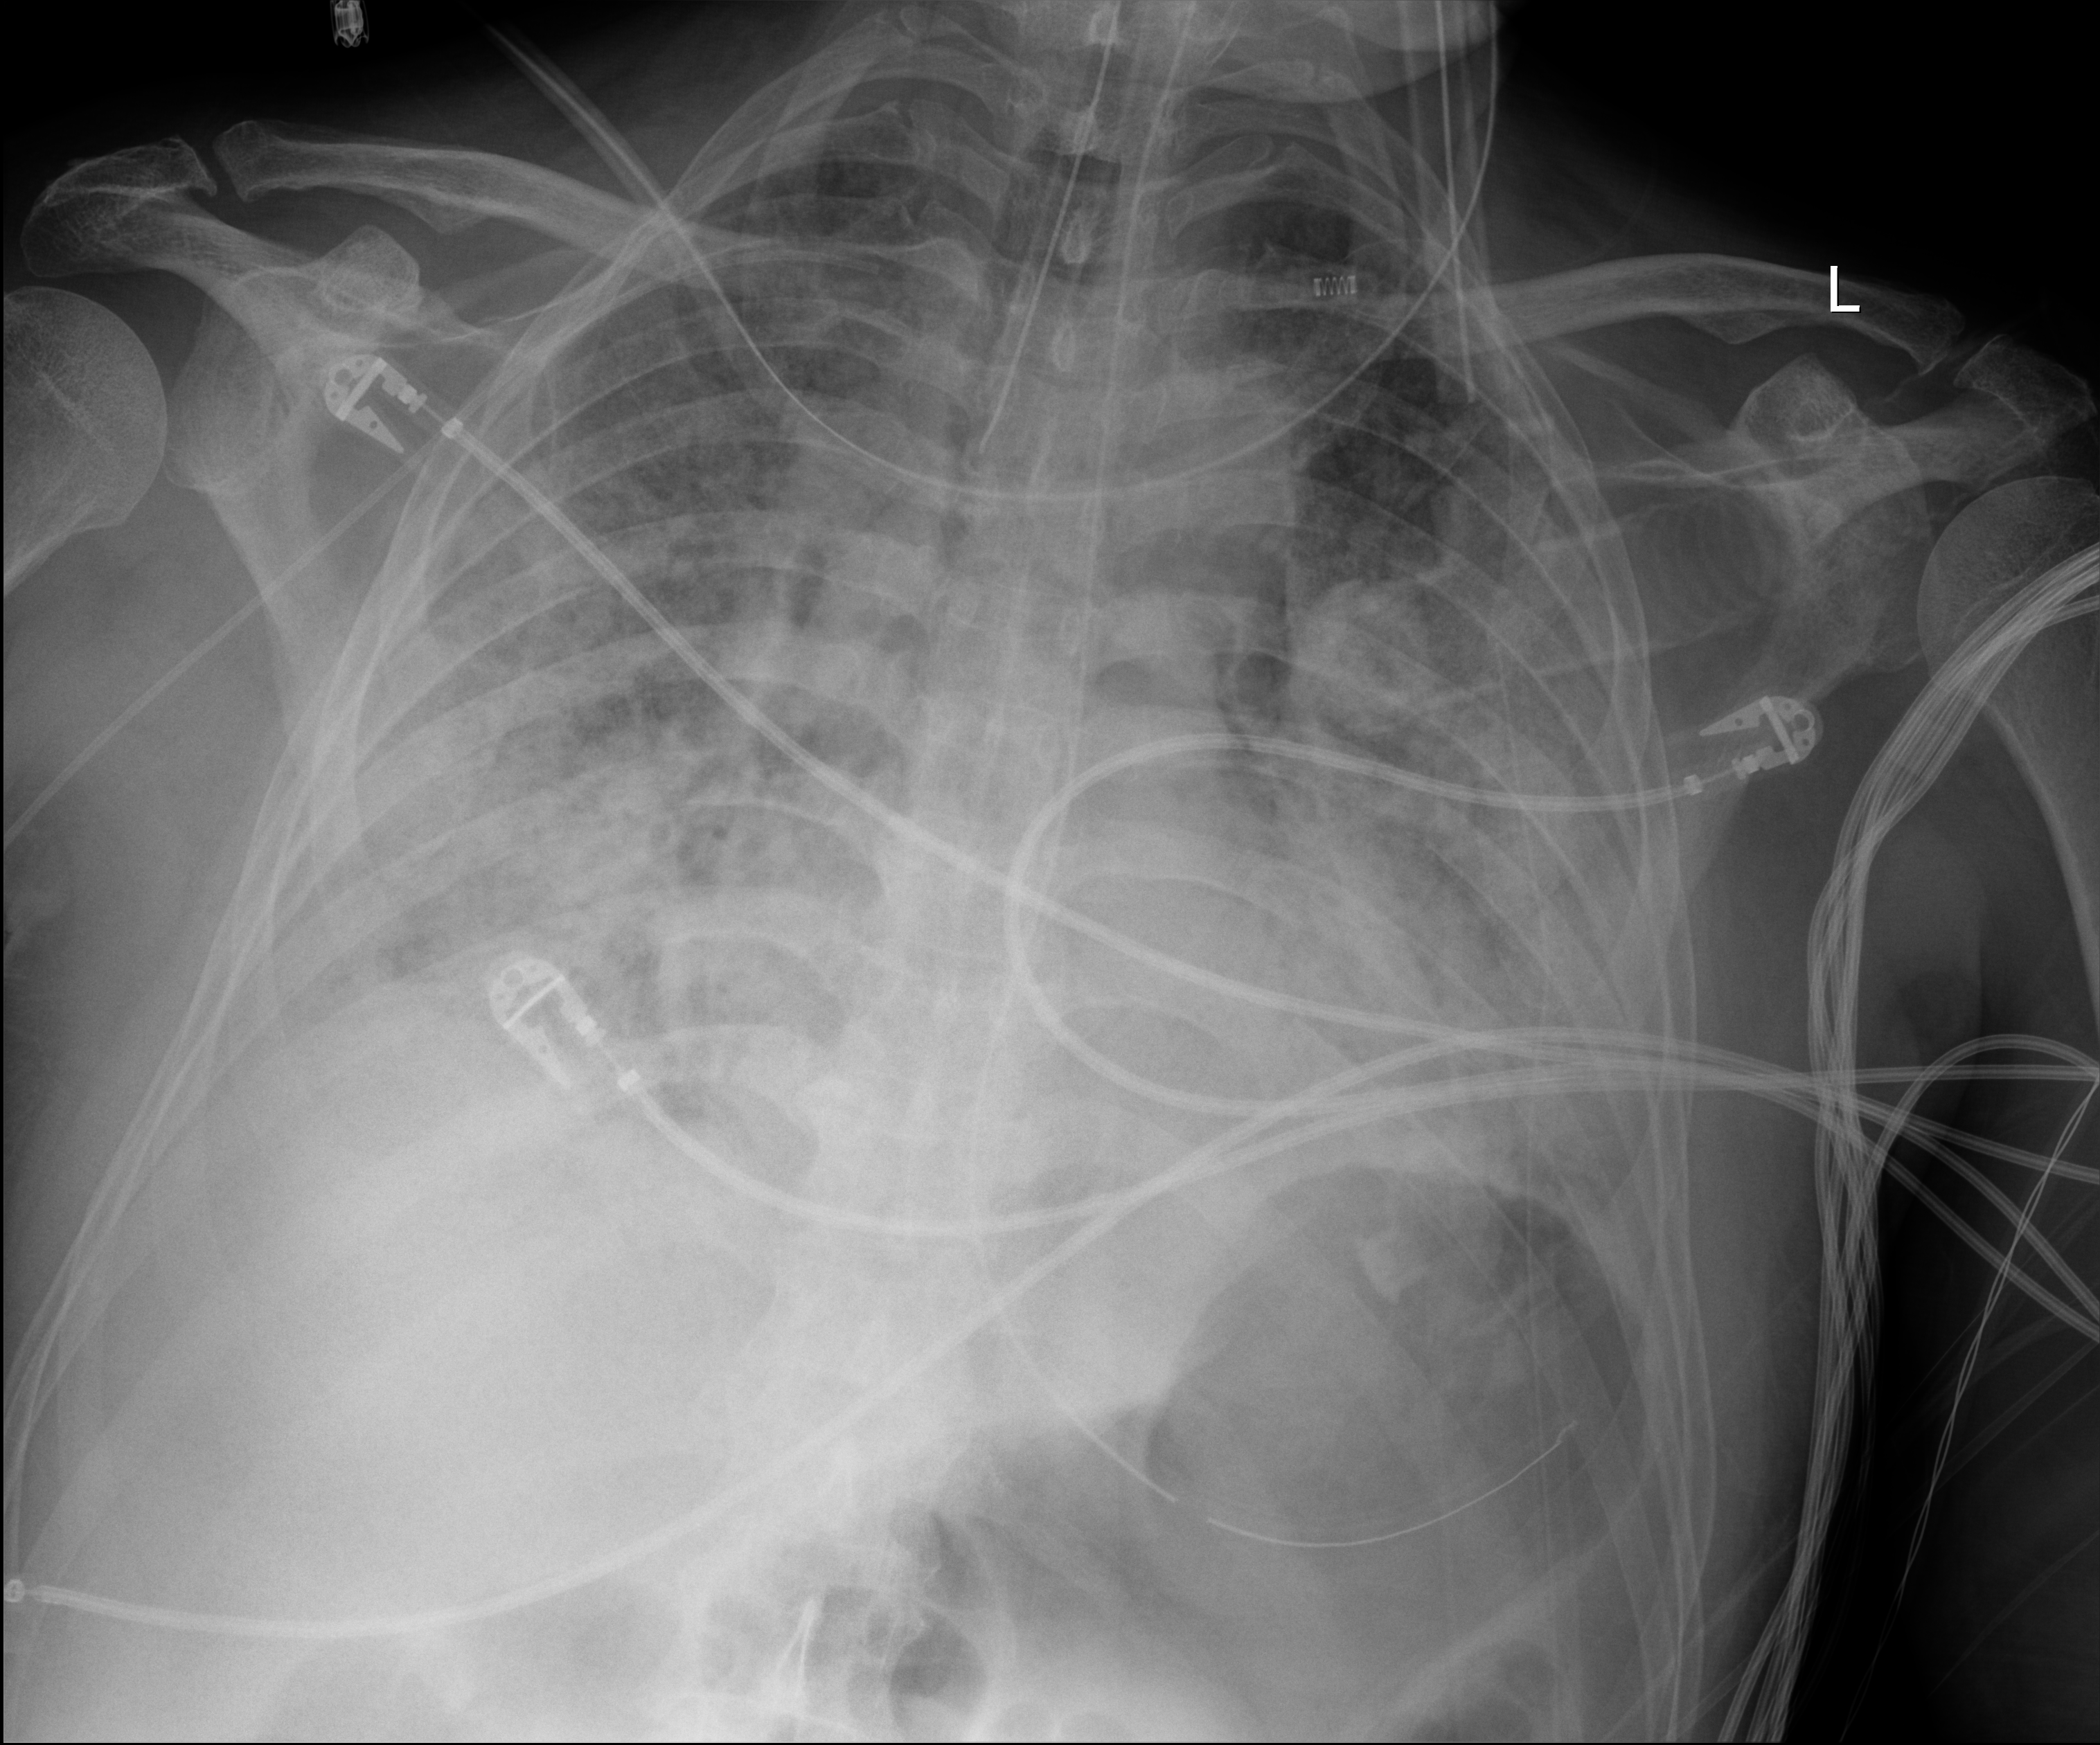
Bedside chest radiograph (digital radiography); anteroposterior (AP) projection. Male patient hospitalised with COVID-19, age 60–74 years.
Hospital-stay facts (about this admission, not read from this image; timing relative to this image not recorded):
- mechanically ventilated during this hospital stay: yes
- length of hospital stay: 37 days